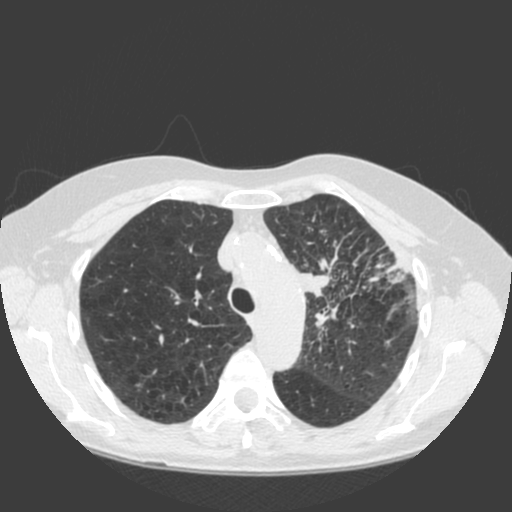
Chest CT (low-dose screening protocol), one axial image. Baseline annual screen. Lung window (W 1500 / L -600 HU). 2 mm slice thickness. Standard (soft-tissue) reconstruction kernel (C). Slice 44 of 184 in the series. 512 × 512 image matrix. Female participant, aged 66 years at enrolment. Current smoker at enrolment.
Lesion marked by an expert reader, bounding box (x1, y1, x2, y2) in pixels: (287, 246, 397, 343). Reader record for this screening exam (exam-level; its link to the box is not recorded): non-calcified nodule or mass ≥4 mm, left upper lobe, 61 × 45 mm, spiculated (stellate) margins, soft tissue attenuation. Official screen result: positive, change unspecified: nodule(s) >= 4 mm or enlarging nodule(s), mass(es), or other non-specific abnormalities suspicious for lung cancer. Lung cancer was diagnosed 19 days after this screen: squamous cell carcinoma, keratinizing, NOS, left upper lobe, left hilum, mediastinum, left main stem bronchus, other location, poorly differentiated (G3), stage IIIB (AJCC 6th edition), 60 mm at pathology.